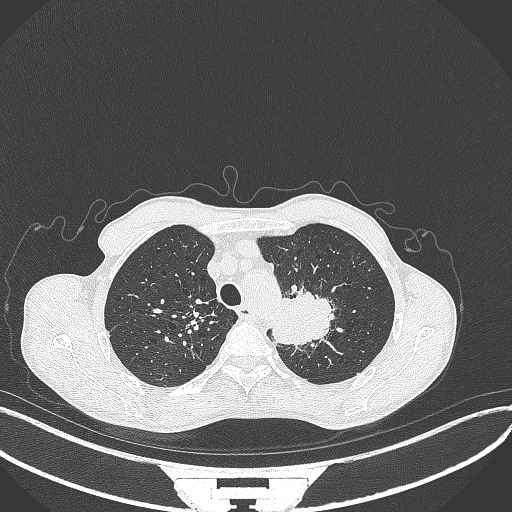
Chest CT, one axial slice. Position 338 of 386 along the scan axis. Reconstruction kernel B70f. 120 kVp. Lung window (W 1500 / L -600 HU). 1 mm slice thickness. 512 × 512 image matrix, field of view 400 × 400 mm. Male patient, age 65 years. Case-level facts recorded for this patient, not image findings: clinical TNM (as recorded): T2b N0 M0.
Outlined on this slice (rectangle marked by the reading radiologist):
- lung tumour (recorded histology: adenocarcinoma): bounding box [x1, y1, x2, y2] px = [269, 282, 337, 350]